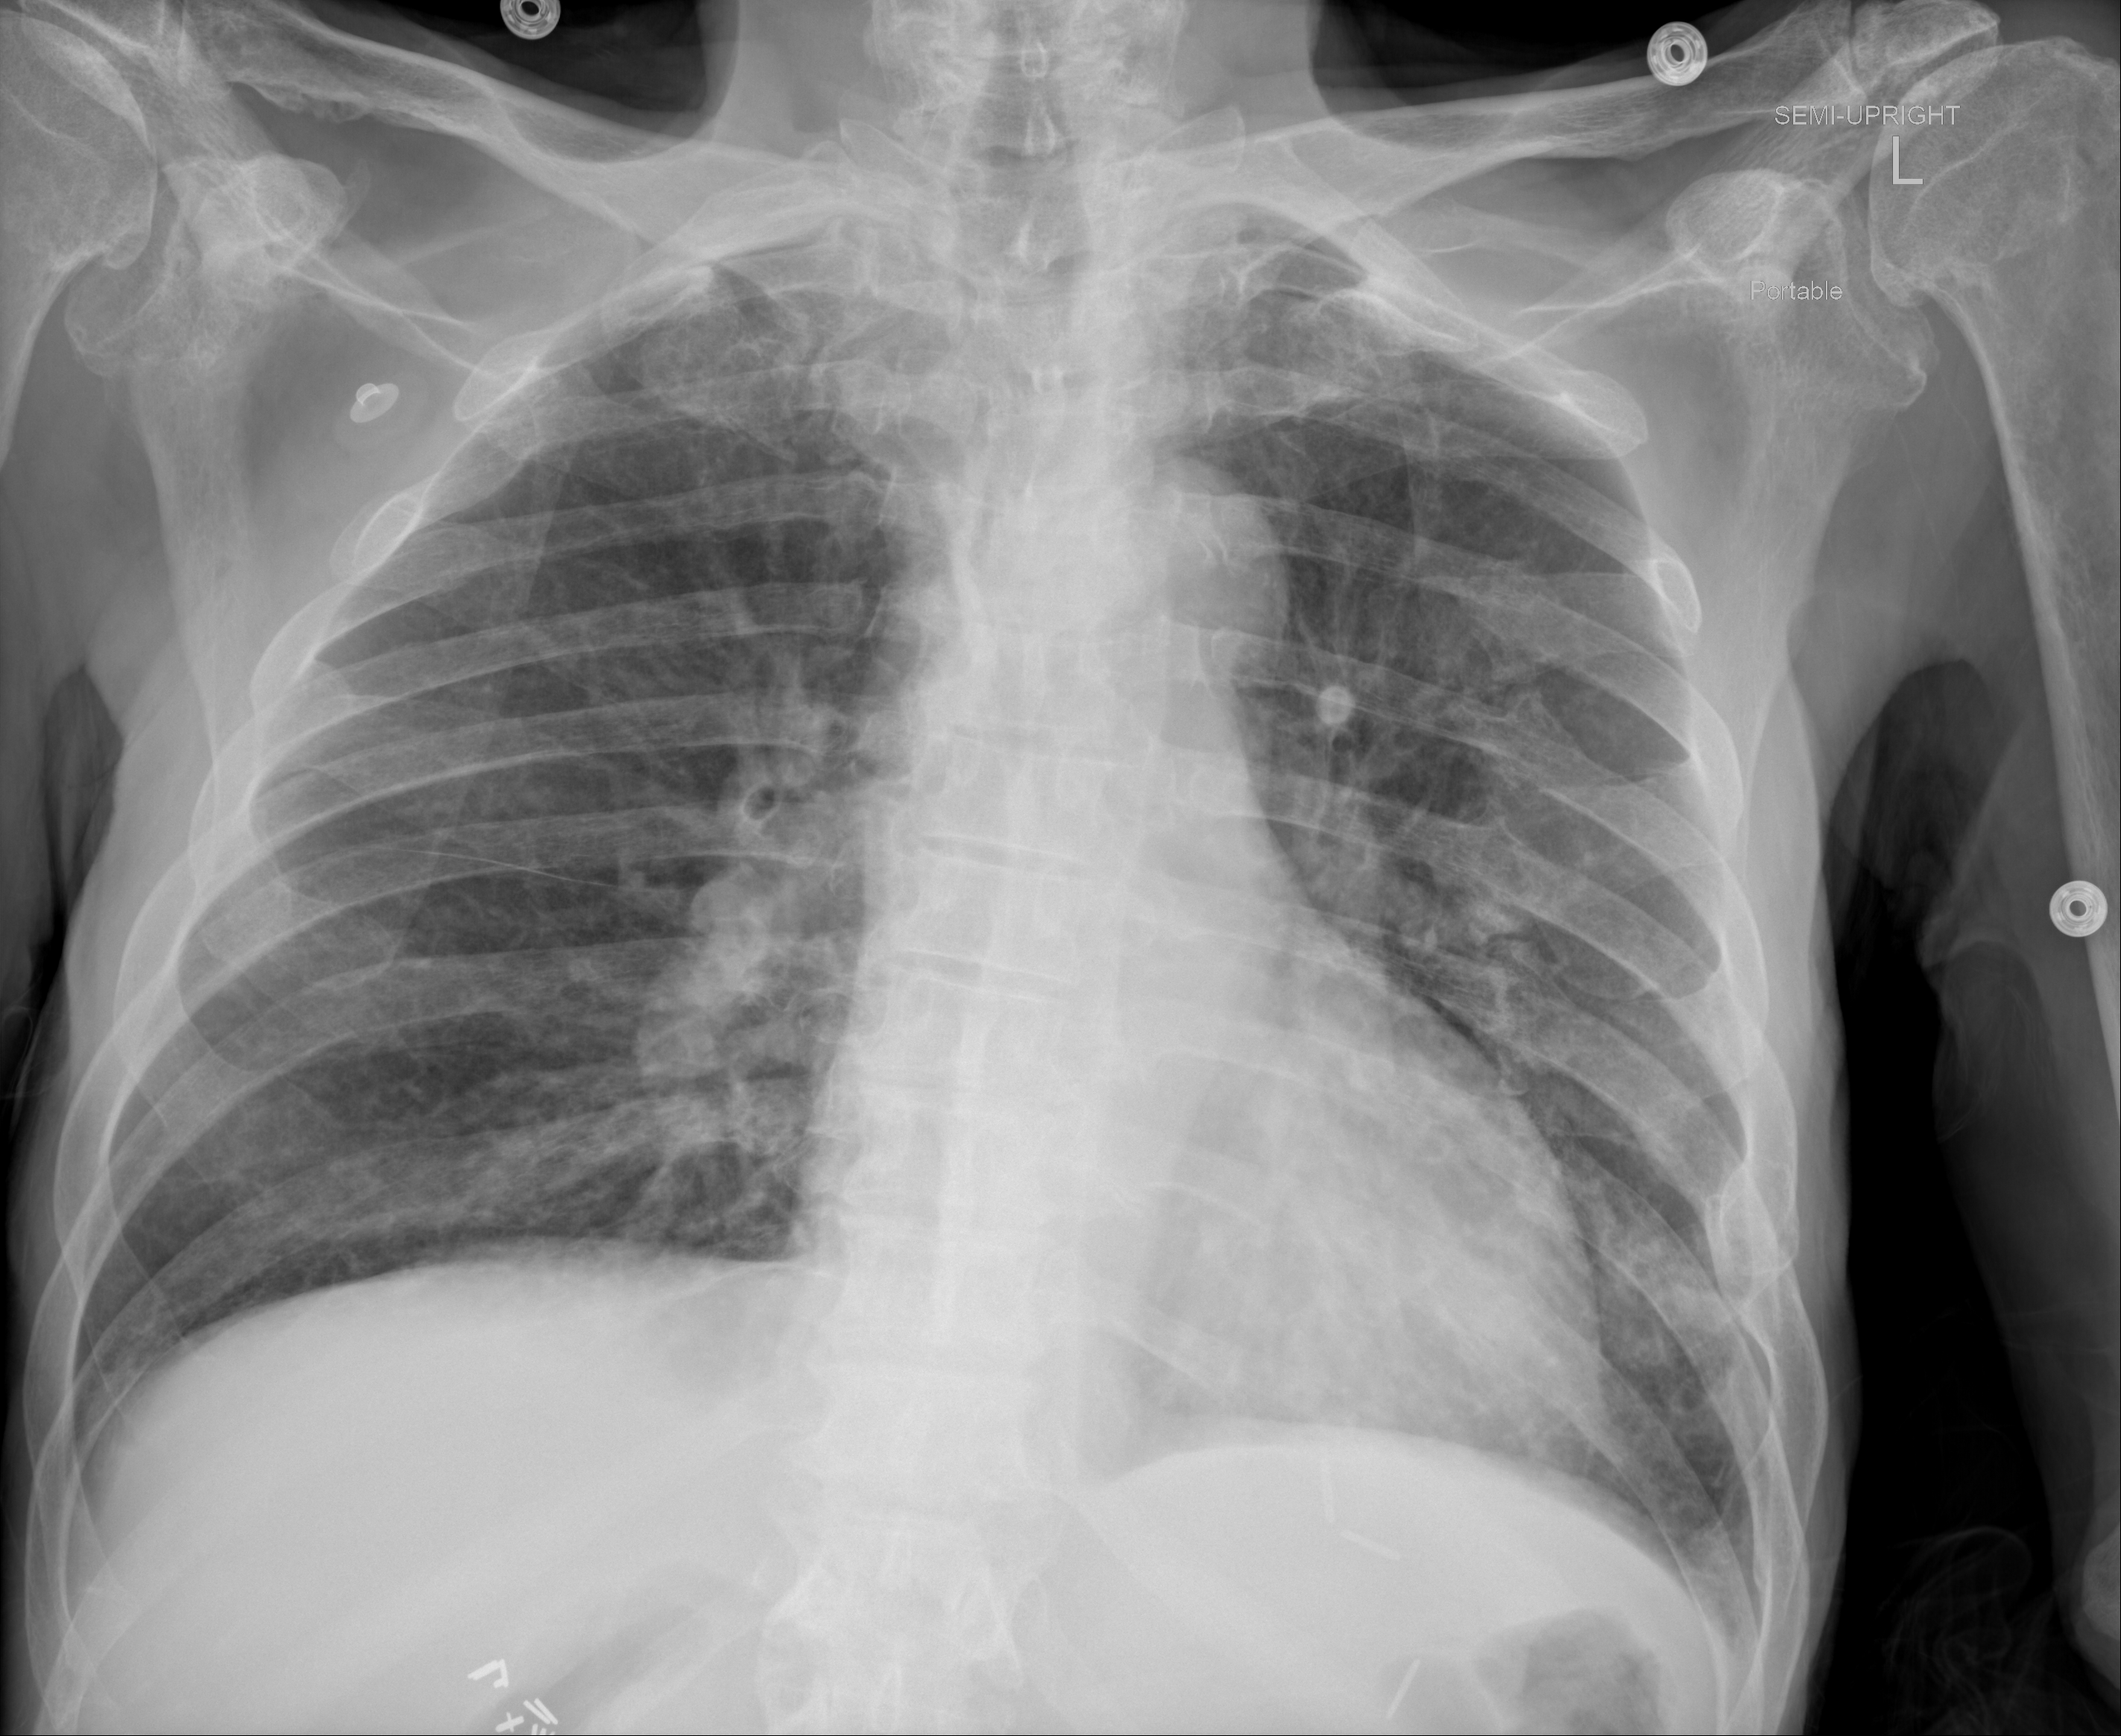
Chest X-ray, lateral projection. Male patient, age 67 years; imaged 2 days after the COVID-19 diagnosis.
Radiologist's key findings for this exam: subtle airspace disease versus chronic parenchymal changes along the left lung base.